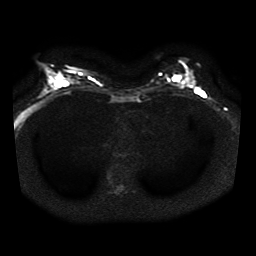
Breast MRI, one axial slice; diffusion-weighted series; image 2 of 4 stored at this slice position (different b-values; order by instance number); 1.5 T; 5 mm slice thickness; 256 × 256 image matrix. Female patient.
Structures marked on this image (manually delineated by an expert):
- tumour on diffusion-weighted imaging: bounding box [x1, y1, x2, y2] px = [186, 80, 193, 86]